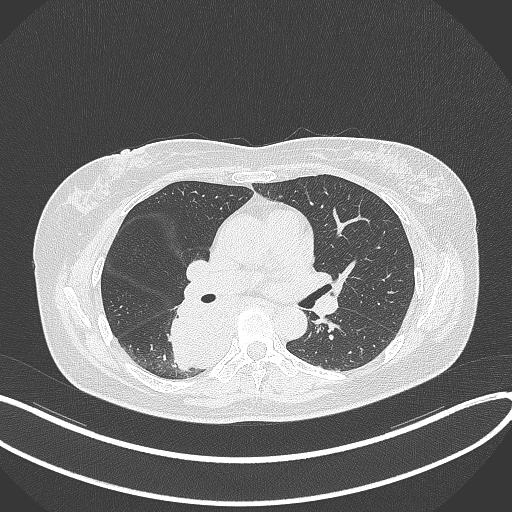
Chest CT, one axial slice; 120 kVp; lung window (W 1500 / L -600 HU); 1 mm slice thickness; 512 × 512 image matrix, field of view 400 × 400 mm. Patient: female, 54 years. Case-level facts recorded for this patient, not image findings: clinical TNM (as recorded): T4 N0 M0.
Outlined on this slice (rectangle marked by the reading radiologist):
- lung tumour (recorded histology: adenocarcinoma): bounding box [x1, y1, x2, y2] px = [168, 295, 233, 373]